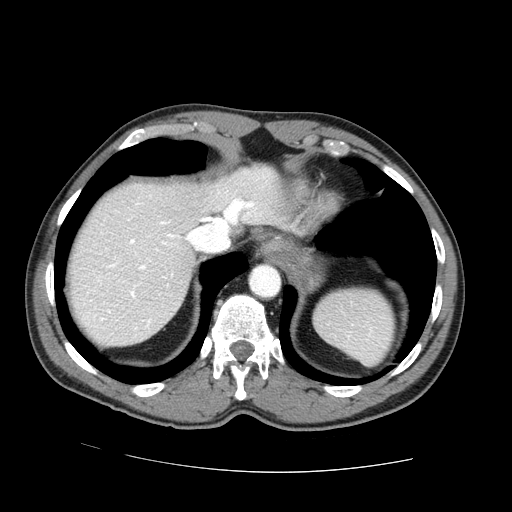
Contrast-enhanced abdominal CT (liver protocol), one axial slice; slice 60 of 73 in the series (ordered by position); reconstruction kernel STANDARD; 100 kVp; one of 2 acquisitions stored at this slice position; soft-tissue window (W 400 / L 40 HU); 512 × 512 image matrix, field of view 380 × 380 mm. From the clinical record (not read from this slice): diagnosis: hepatocellular carcinoma (patient treated with transarterial chemoembolisation; whether this scan precedes or follows treatment is not stated here); TNM stage (as recorded): Stage-IVA; Child-Pugh class: A; tumour differentiation: no biopsy.
Annotated regions visible in this slice (semi-automatic segmentation, software-assisted and operator-edited):
- abdominal aorta: box from (x=251, y=265) to (x=280, y=298) px
- liver parenchyma outside the tumour (the mass and vessels are separate outlines, so this box may not span the whole liver): (x=70, y=166)–(x=306, y=346)
- liver vessels: (x=101, y=199)–(x=254, y=322)